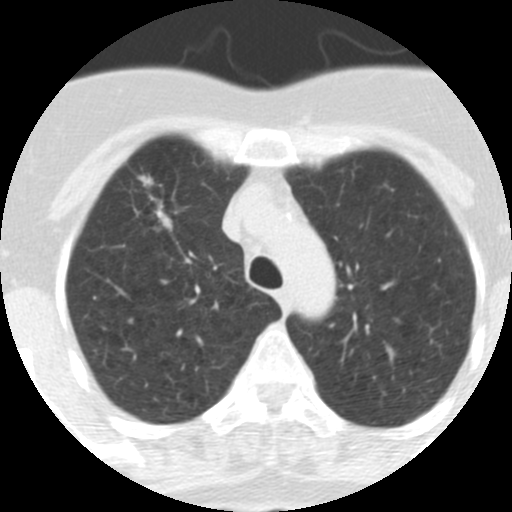
Axial slice from a low-dose chest CT screening exam. First (baseline) screen. Lung window (W 1500 / L -600 HU). 2.5 mm slice thickness. Slice 69 of 313 in the series. Female participant, aged 62 years at enrolment. Current smoker at enrolment.
Expert-annotated lung lesion, bounding box [x1, y1, x2, y2] px = [116, 164, 185, 234]. Screening reader's record for this exam (one nodule recorded; not confirmed to be the boxed lesion): non-calcified nodule or mass ≥4 mm, right upper lobe, 9 × 7 mm, spiculated (stellate) margins, soft tissue attenuation. Official screen result: positive, change unspecified: nodule(s) >= 4 mm or enlarging nodule(s), mass(es), or other non-specific abnormalities suspicious for lung cancer. Participant outcome: lung cancer diagnosed 126 days after this screen — adenocarcinoma, NOS, right upper lobe, moderately differentiated (G2), stage IA (AJCC 6th edition), 18 mm at pathology.